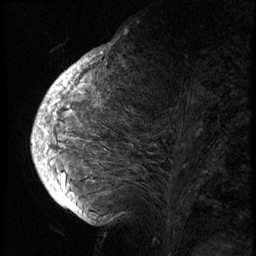
Breast MRI (dynamic contrast-enhanced), one sagittal slice; position 31 of 74 along the scan axis; 3 images stored at this slice position (order not interpretable as contrast timing); 1.5 T; TE 4.2 ms, TR 8.9 ms; 2.5 mm slice thickness; 256 × 256 image matrix, field of view 200 × 200 mm. Patient: female, 57 years. From the clinical record (not read from this slice): setting: breast cancer imaged before/during neoadjuvant chemotherapy; receptor status: HER2-positive.
Structures marked on this image (semi-automatically segmented with operator editing):
- analysis volume of interest (the breast-tissue region the enhancement analysis was run in; not a lesion): bounding box [x1, y1, x2, y2] px = [40, 62, 230, 175]
- tumour enhancement mask (voxels above the 140 % enhancement threshold inside the analysis volume of interest): [42, 62, 90, 164]